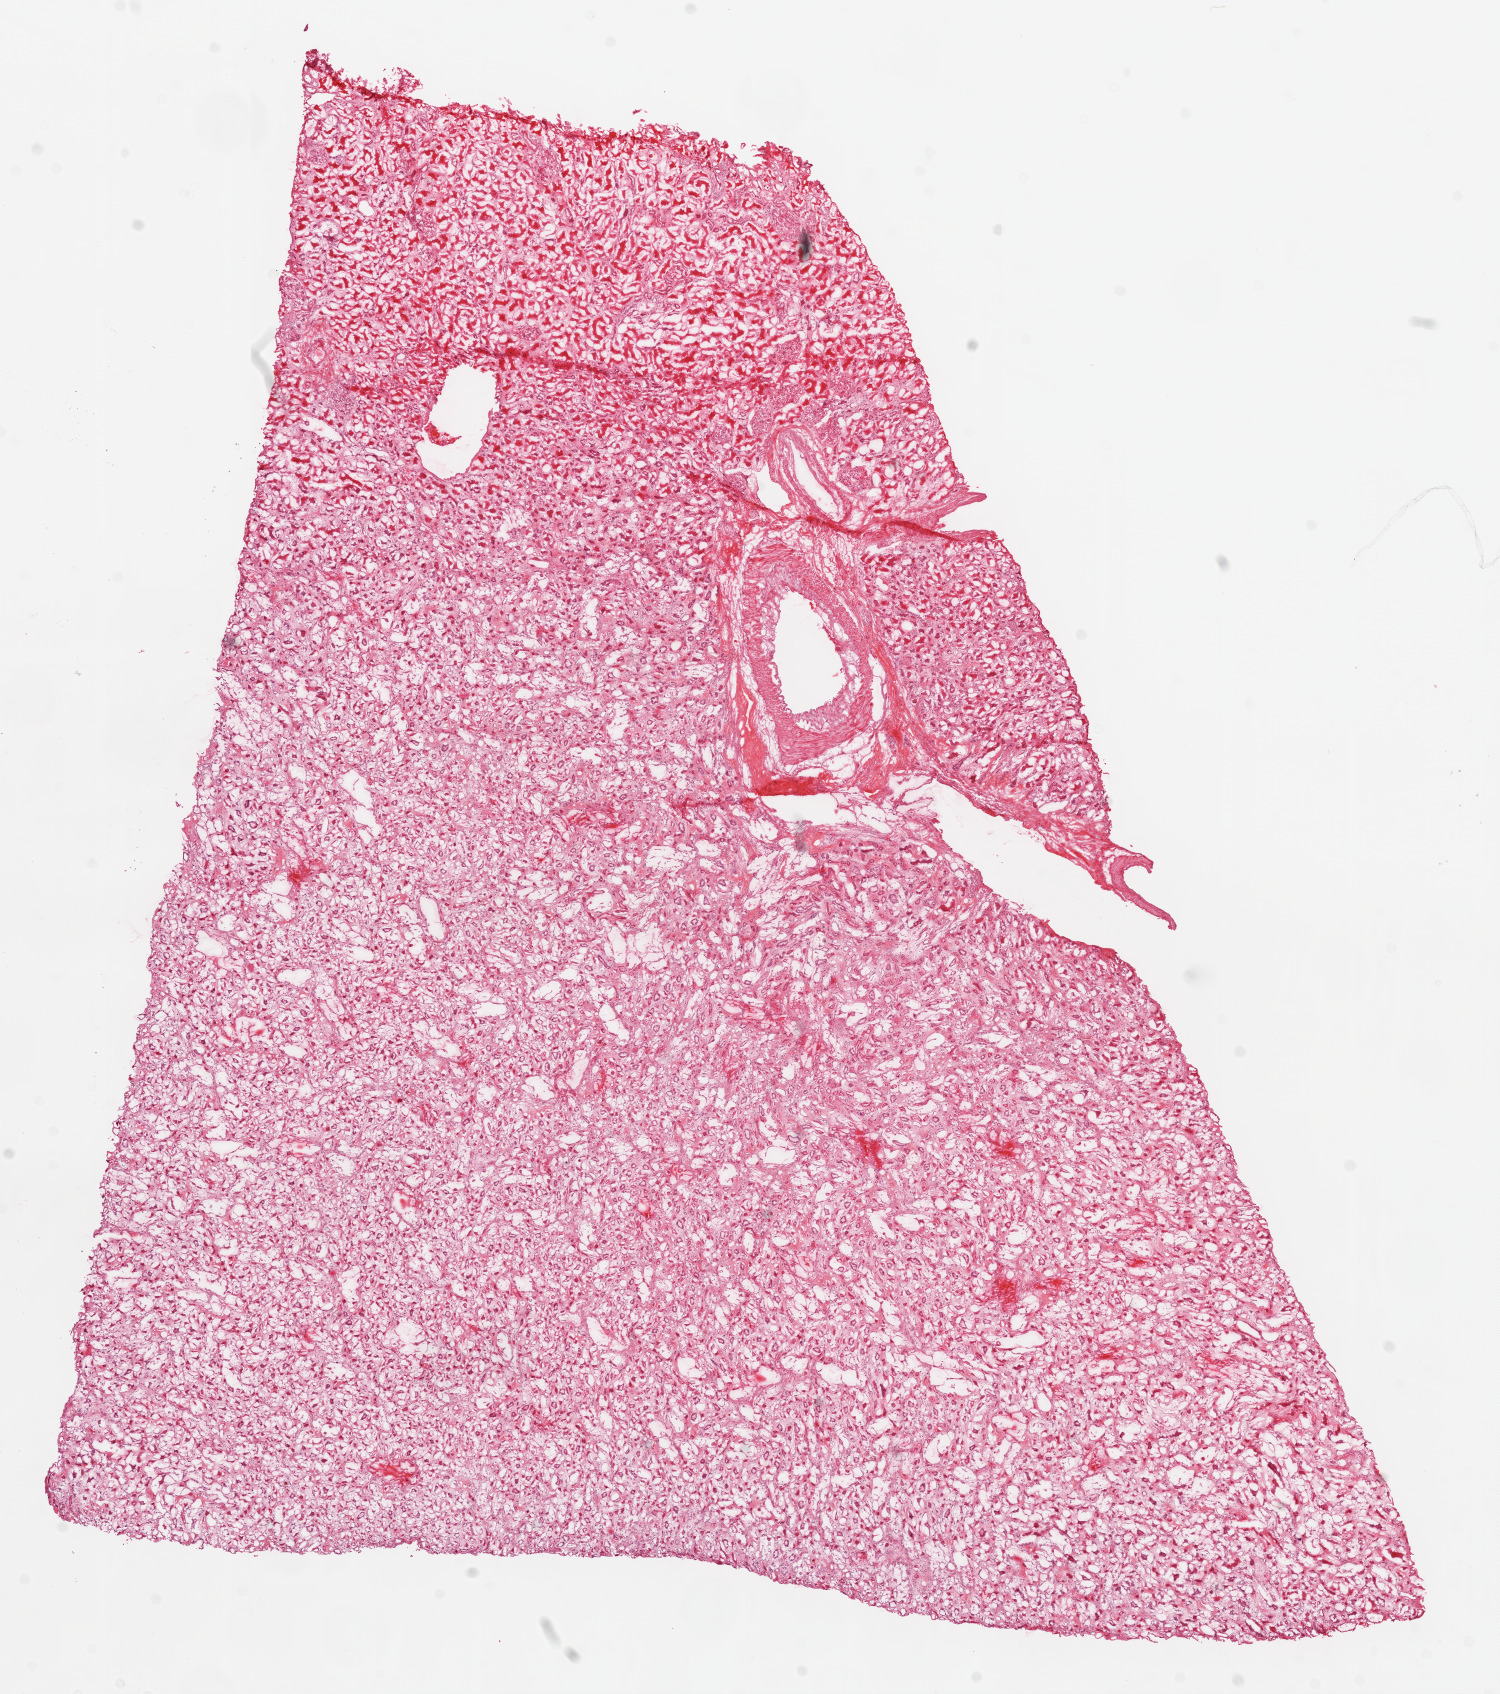
H&E-stained whole-slide image — shown as a low-resolution overview of the whole scanned area (about 12.0 x 13.6 mm, slide scanned at 20x); frozen section from the top of the tissue portion; kidney, solid tissue normal (non-tumour tissue) sample. Male, age 52 years at initial diagnosis.
This section: solid tissue normal sample (biorepository sample class). Patient diagnosis: Clear cell adenocarcinoma, NOS.